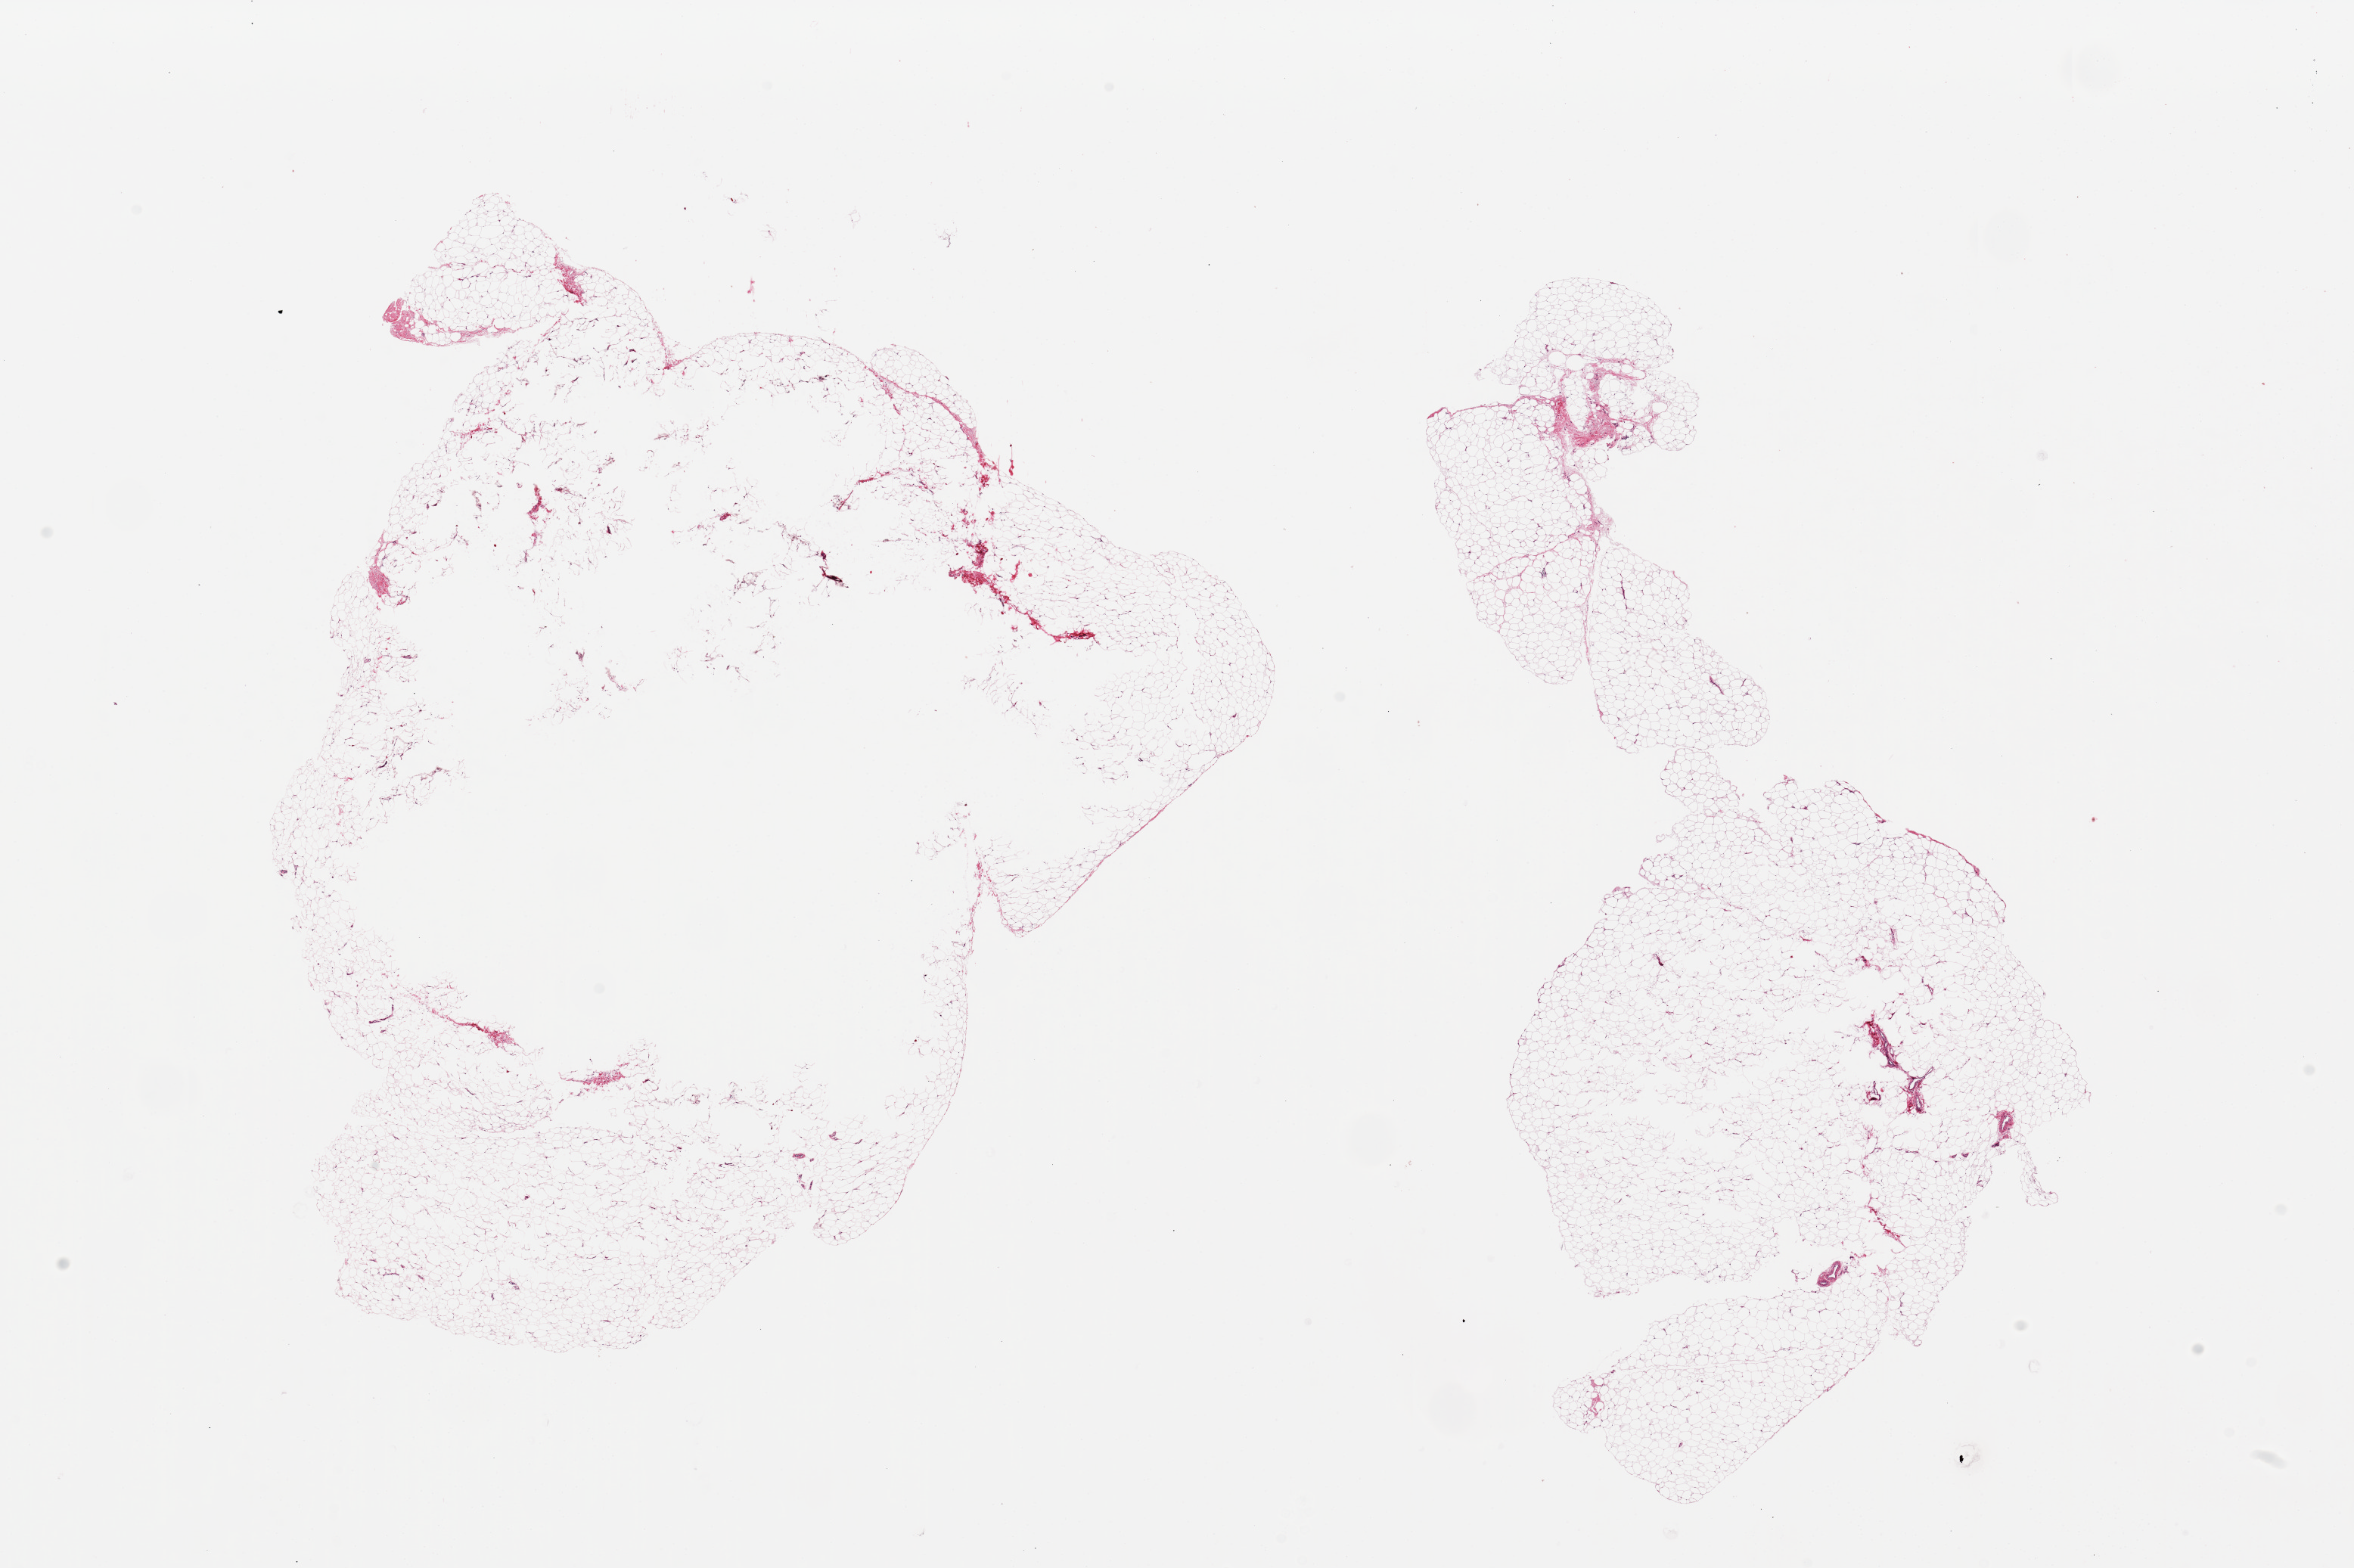
Whole-slide image, H&E stain, shown as a low-resolution overview of the whole scanned area (about 24.6 x 16.4 mm), PAXgene-fixed, paraffin-embedded tissue, section of adipose tissue (target tissue), donor tissue sample. Donor: female.
Reviewer comment on this tissue sample: 2 pieces, 11x9.5 & 10x7mm; larger piece has central hollow defect >50% of aliquot.